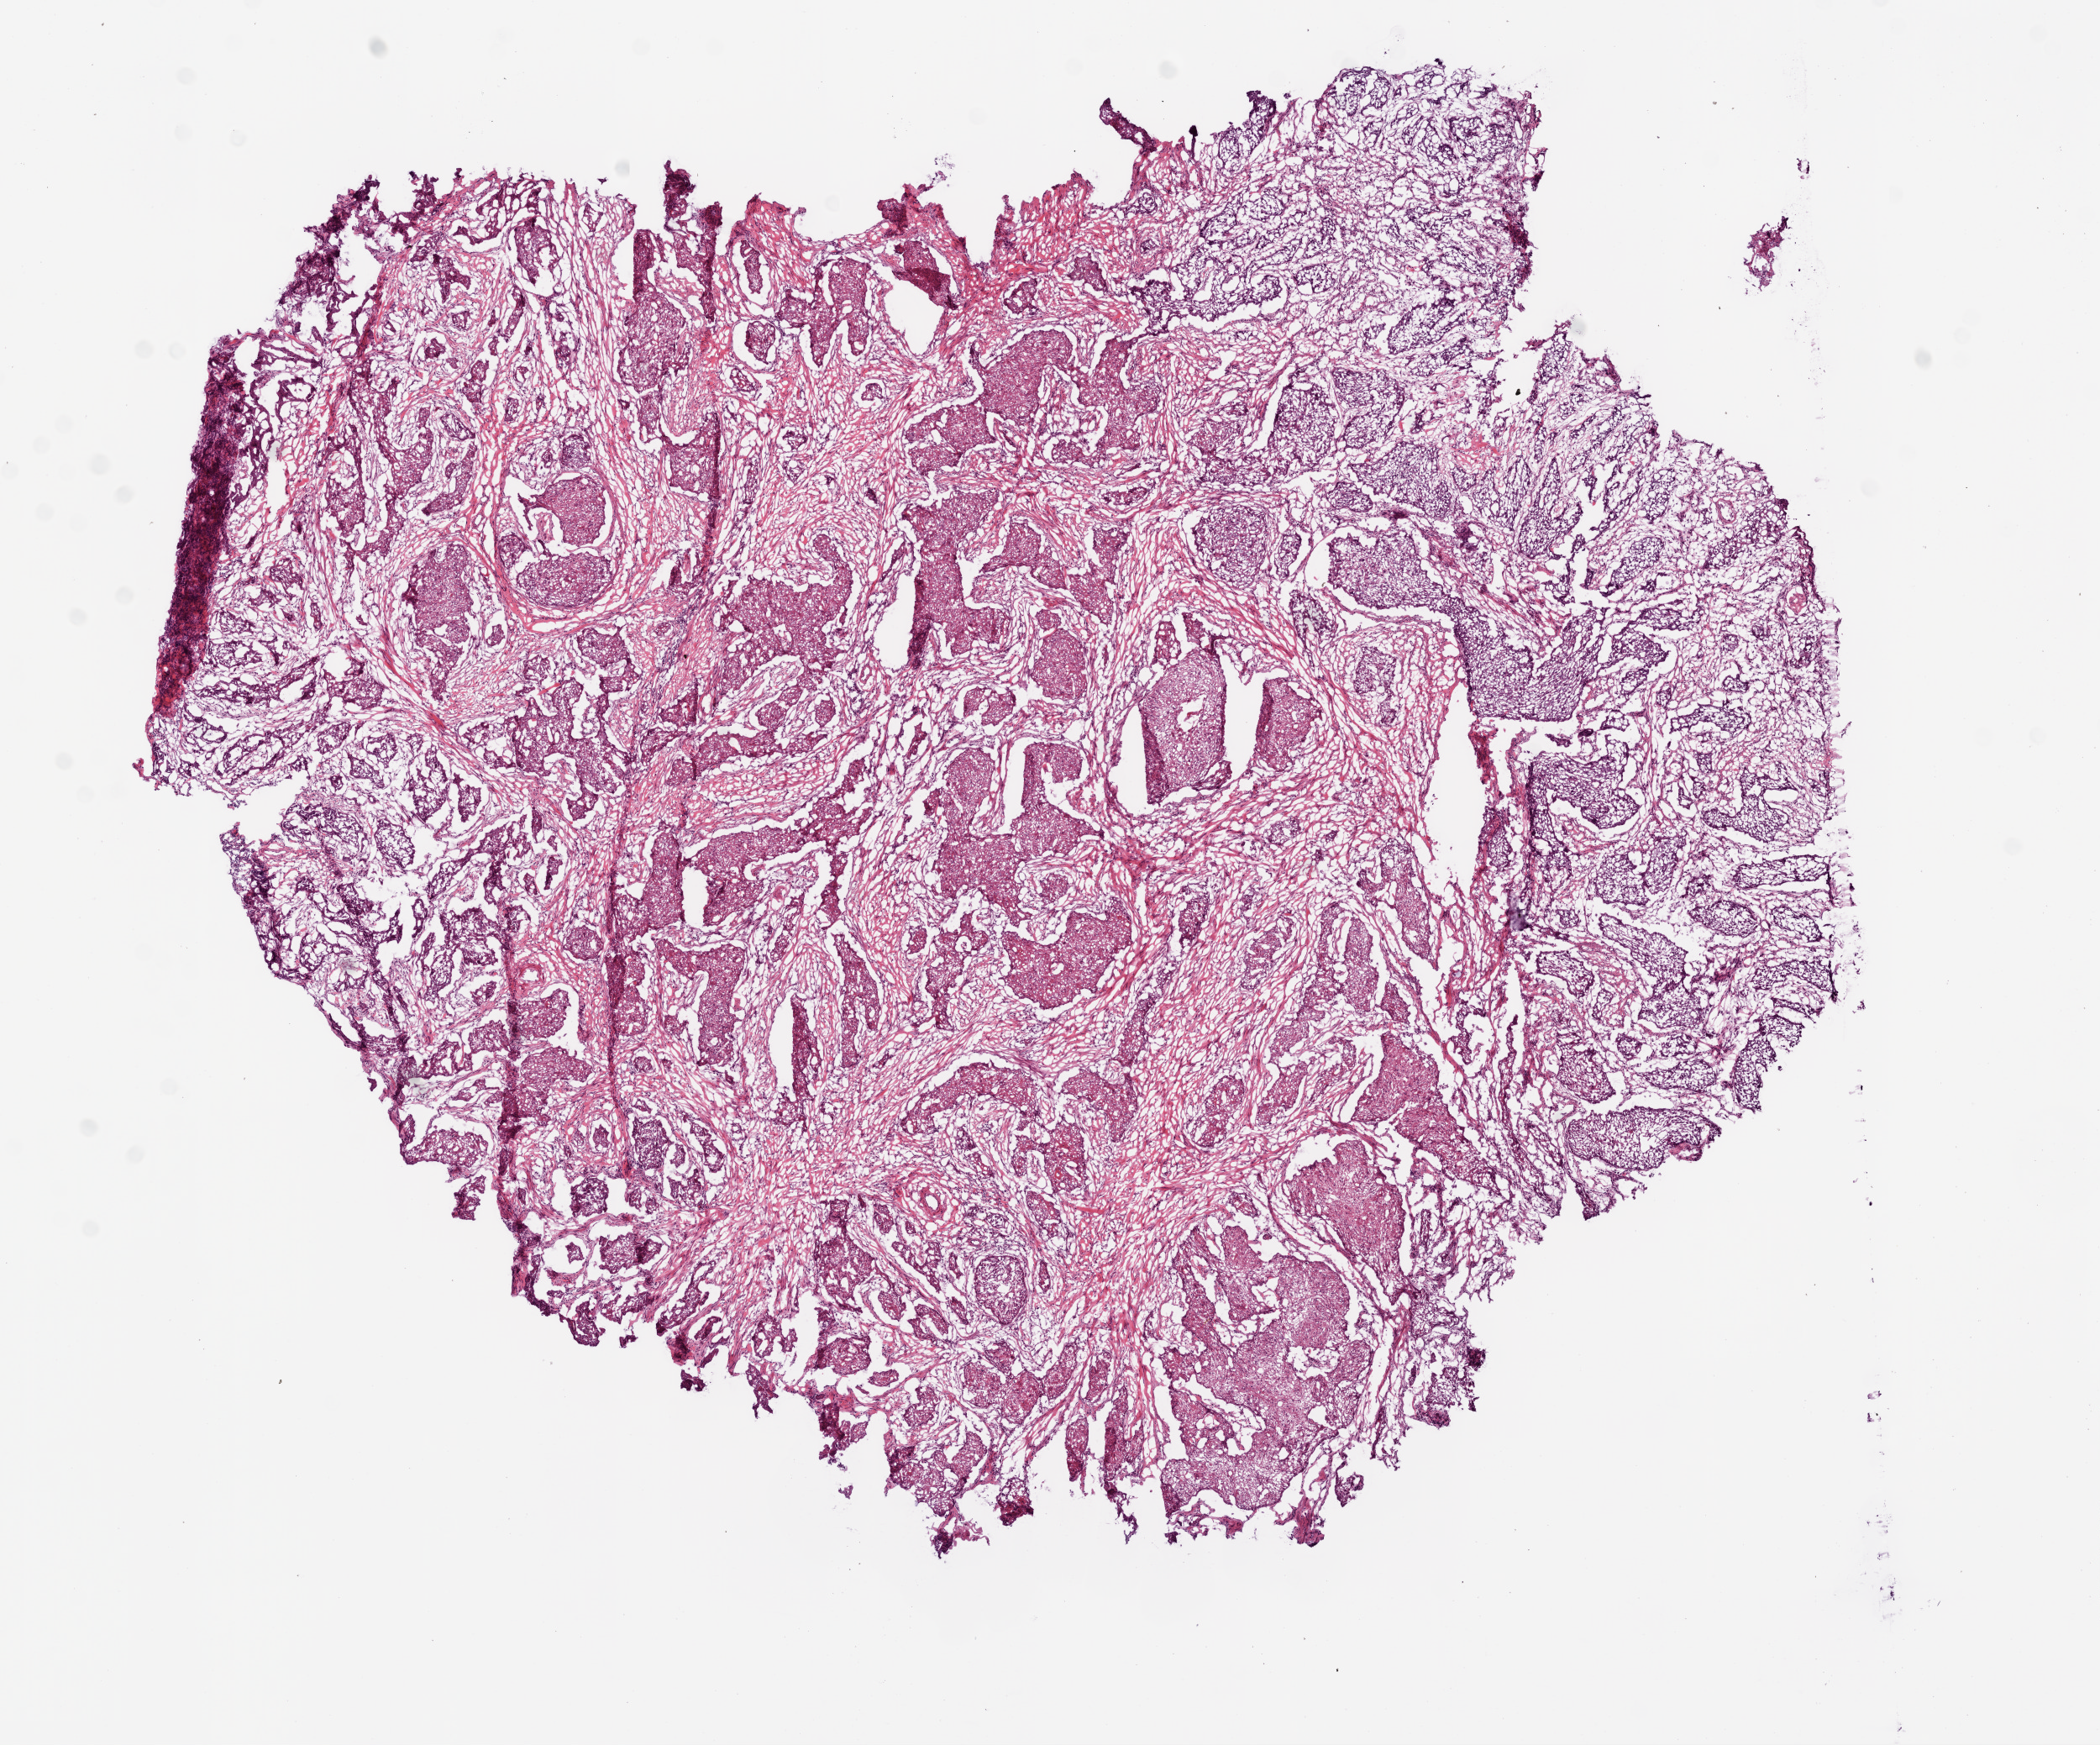
Digitized Hematoxylin and eosin (H&E) stained tissue section (whole slide), whole scanned area (about 10.0 x 8.3 mm) shown as a low-resolution overview, frozen section from the bottom of the tissue portion, primary tumour sample from the head and neck. Male, age 80 years at initial diagnosis. Histologic grade: G2 (moderately differentiated). Pathologist review of this section (percent, as recorded): tumour cells 80%, tumour nuclei 80%, normal cells 0%, stromal cells 20%, necrosis 0%.
• AJCC pathologic stage: IVA
• pathologic diagnosis: Squamous cell carcinoma, NOS (larynx, NOS)